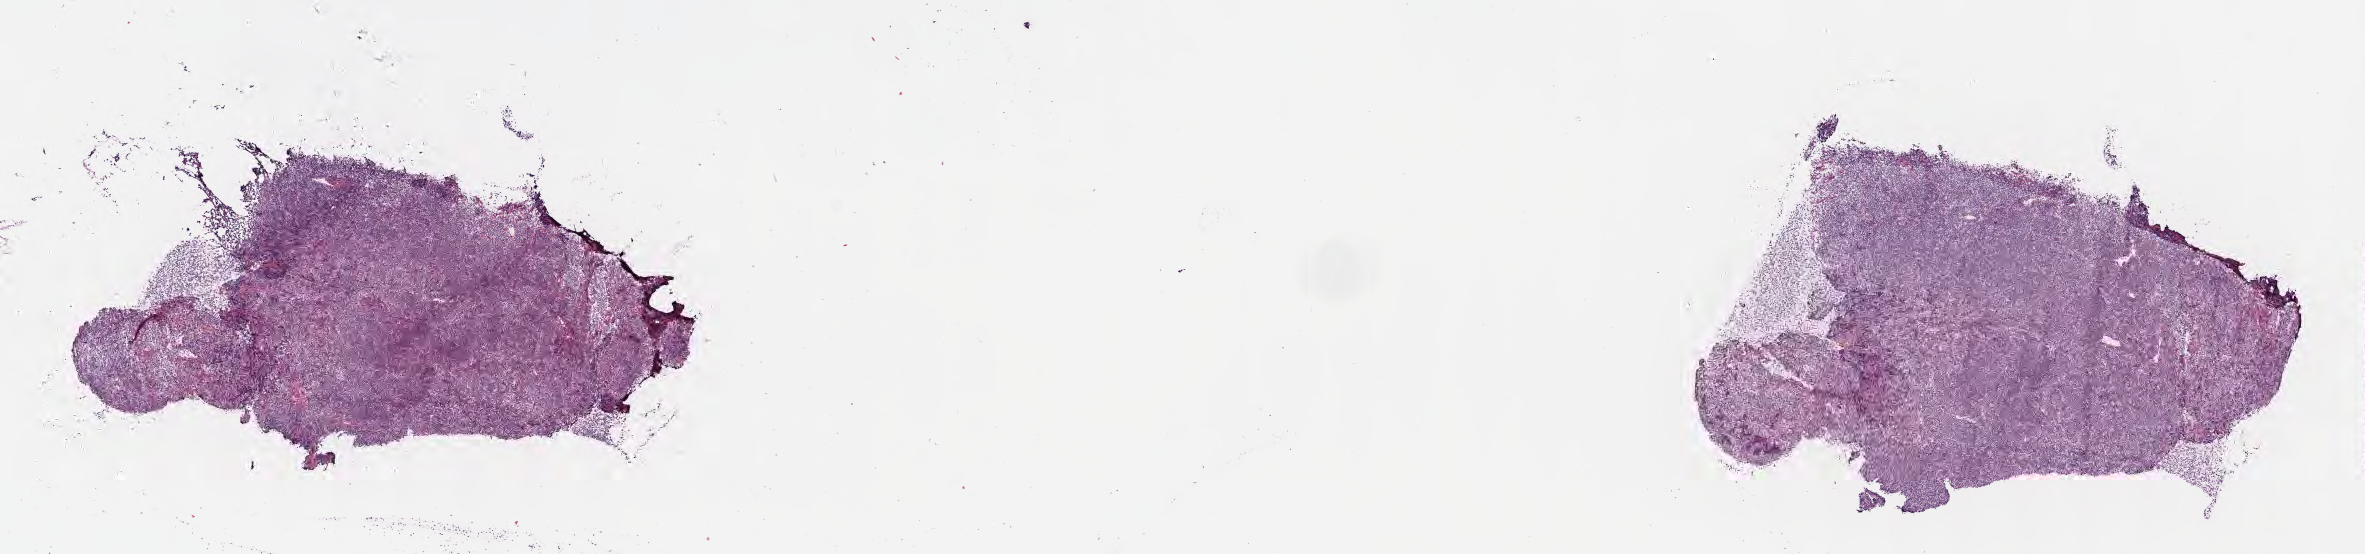
H&E whole-slide image, whole scanned area (about 19.1 x 4.5 mm) shown as a low-resolution overview; frozen section; primary tumor; anatomic site: cranium. Female patient; age at initial diagnosis 3 years. Pathologist review of this section (percent, as recorded): tumor cells 95%, tumor nuclei 95%.
Histologic diagnosis: Burkitt lymphoma, NOS.